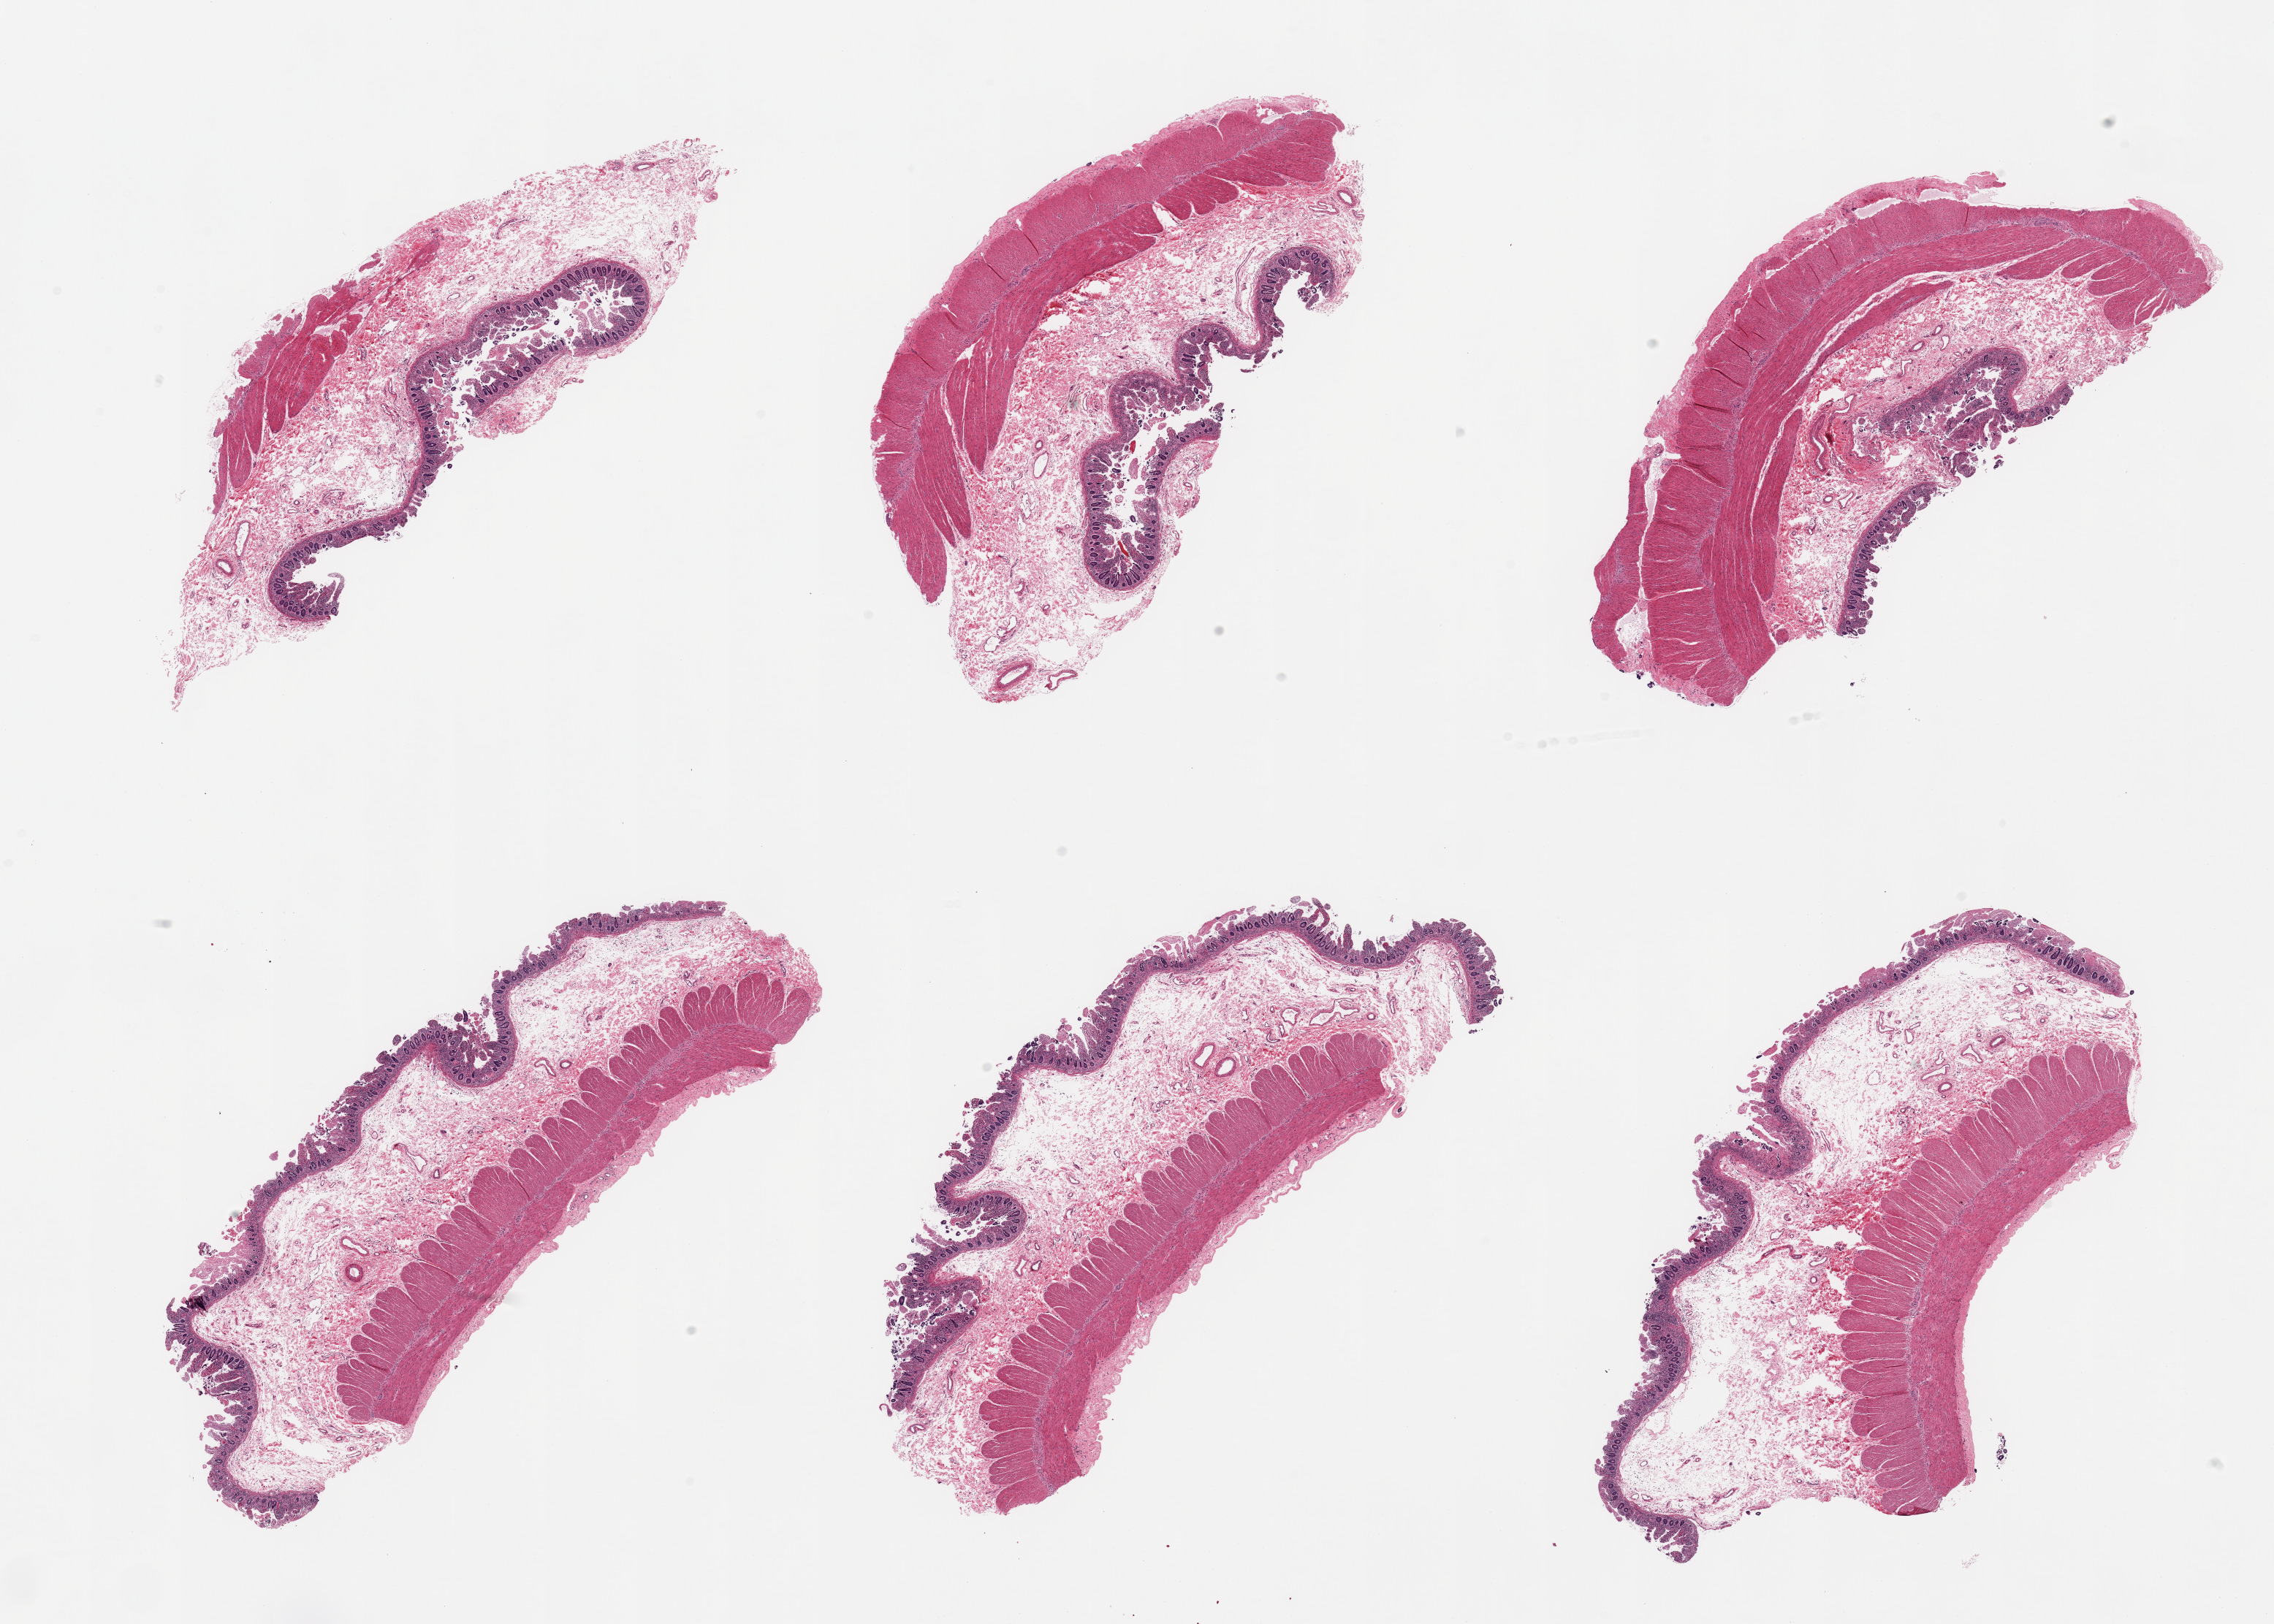
Hematoxylin and eosin (H&E) whole-slide image, whole scanned area (about 24.6 x 17.6 mm, from a 20x scan) shown as a low-resolution overview. PAXgene-fixed paraffin-embedded (PFPE) section. Sampled site (target tissue): ileum. Tissue donor sample.
Pathologist's review note for this sample: 6 pieces; full thickness sections, no significant lymphoid tissue.